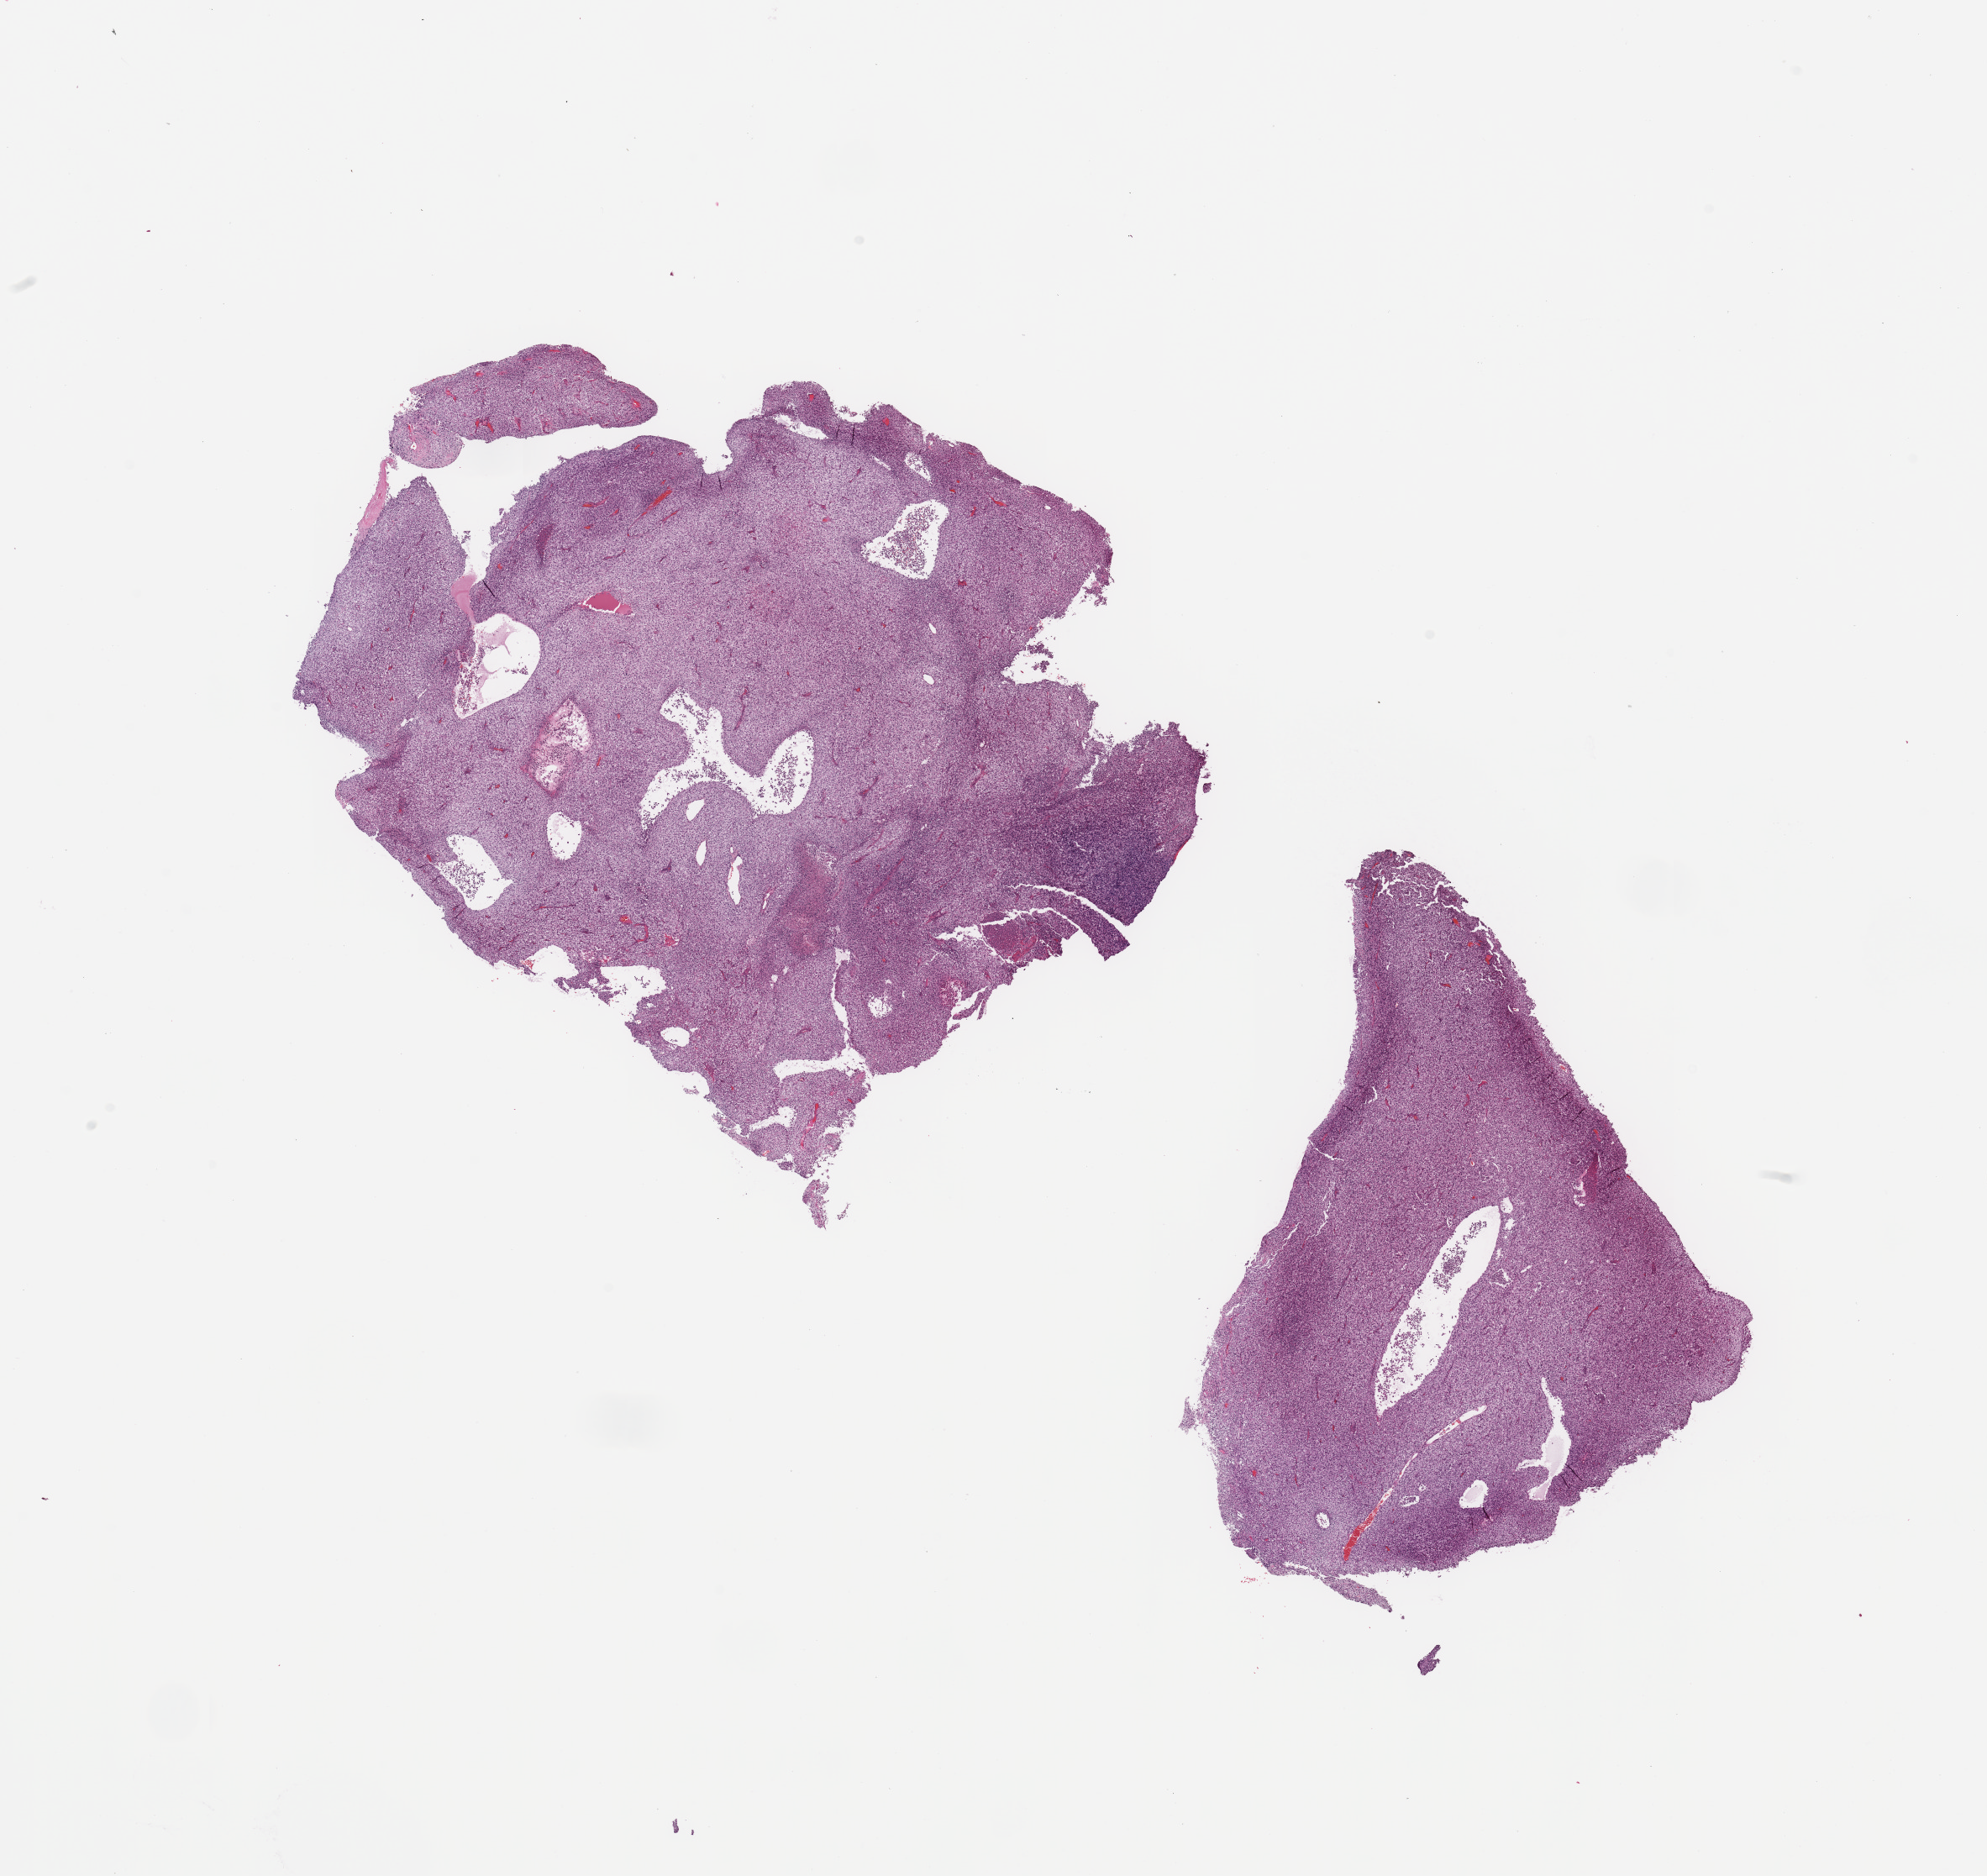
Whole-slide histology image, H&E, shown as a low-resolution overview of the whole scanned area (about 18.7 x 17.7 mm, slide scanned at 20x), kidney, tumour tissue. Male, 61 y/o. Histologic grade: G4 (undifferentiated).
• histologic diagnosis: Renal cell carcinoma, NOS
• primary tumour site (as recorded): upper pole
• AJCC pathologic stage: IV